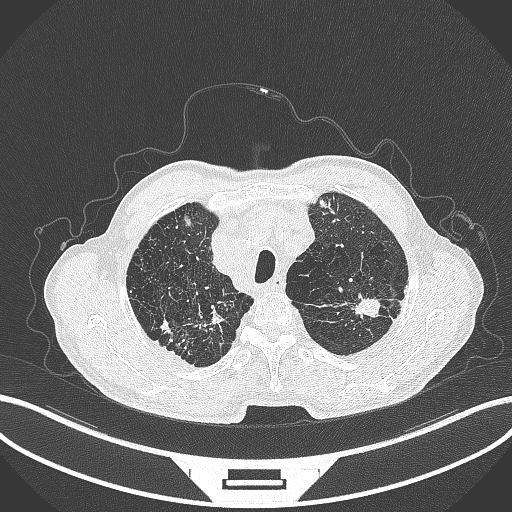
Chest CT, one axial slice. Position 373 of 463 along the scan axis. Reconstruction kernel B70f. 120 kVp. Lung window (W 1500 / L -600 HU). 512 × 512 image matrix, field of view 400 × 400 mm. Patient: male, 74 years. Case-level facts recorded for this patient, not image findings: clinical TNM (as recorded): T2a N1 M0.
Annotated regions visible in this slice (rectangle marked by the reading radiologist):
- lung tumour (recorded histology: adenocarcinoma): bounding box <348,294,381,321> (left, top, right, bottom; pixels)